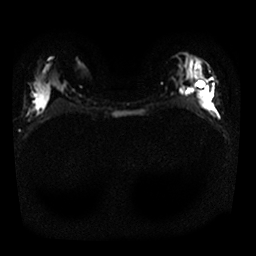
Breast MRI, one axial slice; position 11 of 25 along the scan axis; diffusion-weighted series; image 2 of 4 stored at this slice position (different b-values; order by instance number); 1.5 T; 4 mm slice thickness; 256 × 256 image matrix, field of view 320 × 320 mm. Female patient.
Outlined on this slice (expert manual segmentation):
- tumour on diffusion-weighted imaging: bounding box [x1, y1, x2, y2] px = [199, 88, 212, 108]